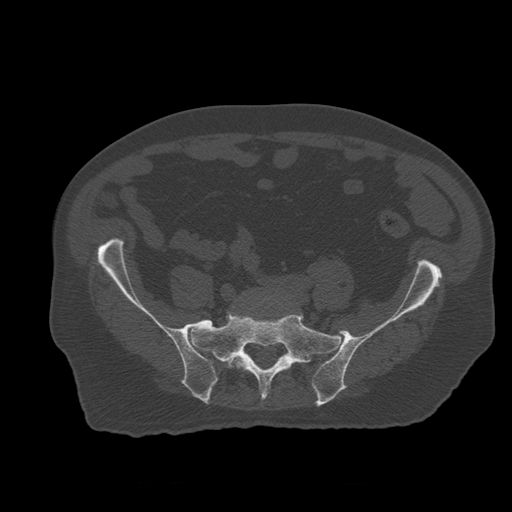
CT including the spine, one axial slice; position 124 of 399 along the scan axis; reconstruction kernel STANDARD; bone window (W 1800 / L 400 HU); 1.25 mm slice thickness; 512 × 512 image matrix. Patient age 73 years. Case-level facts recorded for this patient, not image findings: primary cancer: prostate; vertebrae with lytic lesions (as recorded): L2.
Structures marked on this image (semi-automatically segmented with operator editing):
- L5 vertebra: bounding box [x1, y1, x2, y2] px = [222, 296, 257, 369]